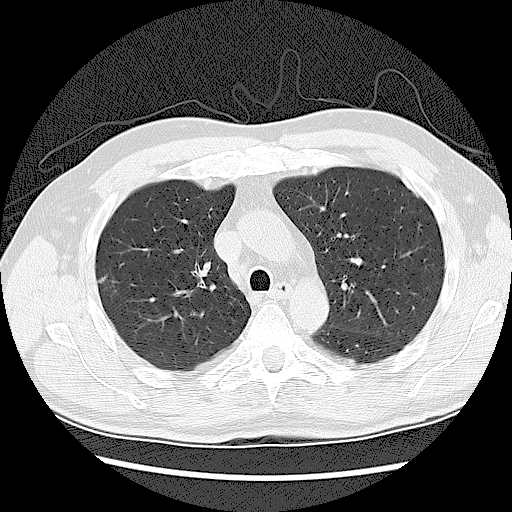
Low-dose screening chest CT, one axial slice; slice 83 of 120 in the series (ordered by position); reconstruction kernel LUNG; 120 kVp; lung window (W 1500 / L -600 HU); 512 × 512 image matrix, field of view 360 × 360 mm.
Annotated regions visible in this slice (manually delineated by an expert):
- lesion 1 (tumor, upper lobe of right lung): bounding box (x1, y1, x2, y2) in pixels: (98, 276, 107, 284)